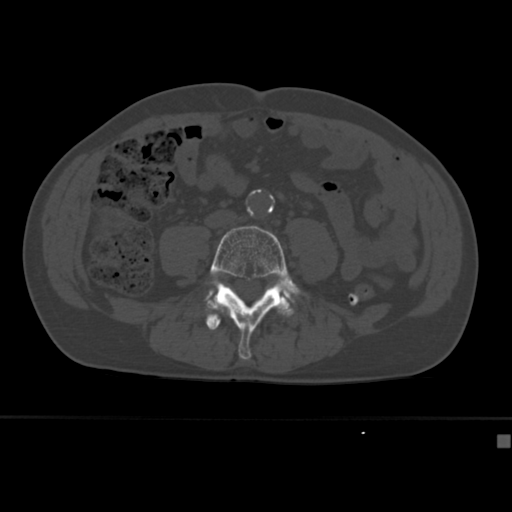
CT including the spine, one axial slice. Position 104 of 430 along the scan axis. Reconstruction kernel Br40s. 120 kVp. Bone window (W 1800 / L 400 HU). 1.5 mm slice thickness. 512 × 512 image matrix. Patient: male, 64 years. Case-level facts recorded for this patient, not image findings: primary cancer: uterus; vertebrae with lytic lesions (as recorded): T1, T4, T5, T7, L5.
Outlined on this slice (semi-automatically segmented with operator editing):
- L4 vertebra: bounding box [x1, y1, x2, y2] px = [204, 225, 310, 361]
- L5 vertebra: [206, 280, 296, 304]